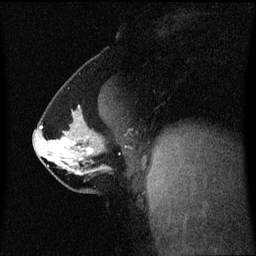
Breast MRI (dynamic contrast-enhanced), one sagittal slice; slice 32 of 60 in the series (ordered by position); dynamic contrast-enhanced series, image 2 of 3 at this slice position (ordered by acquisition); 1.5 T; TE 4.2 ms, TR 8.4 ms; 2 mm slice thickness; 256 × 256 image matrix, field of view 210 × 210 mm. Patient: female, 40 years. From the clinical record (not read from this slice): setting: breast cancer imaged before/during neoadjuvant chemotherapy; receptor status: triple-negative.
Outlined on this slice (semi-automatic segmentation, software-assisted and operator-edited):
- analysis volume of interest (the breast-tissue region the enhancement analysis was run in; not a lesion): box from (x=33, y=112) to (x=112, y=188) px
- tumour enhancement mask (voxels above the 70 % enhancement threshold inside the analysis volume of interest): (x=51, y=138)–(x=94, y=154)